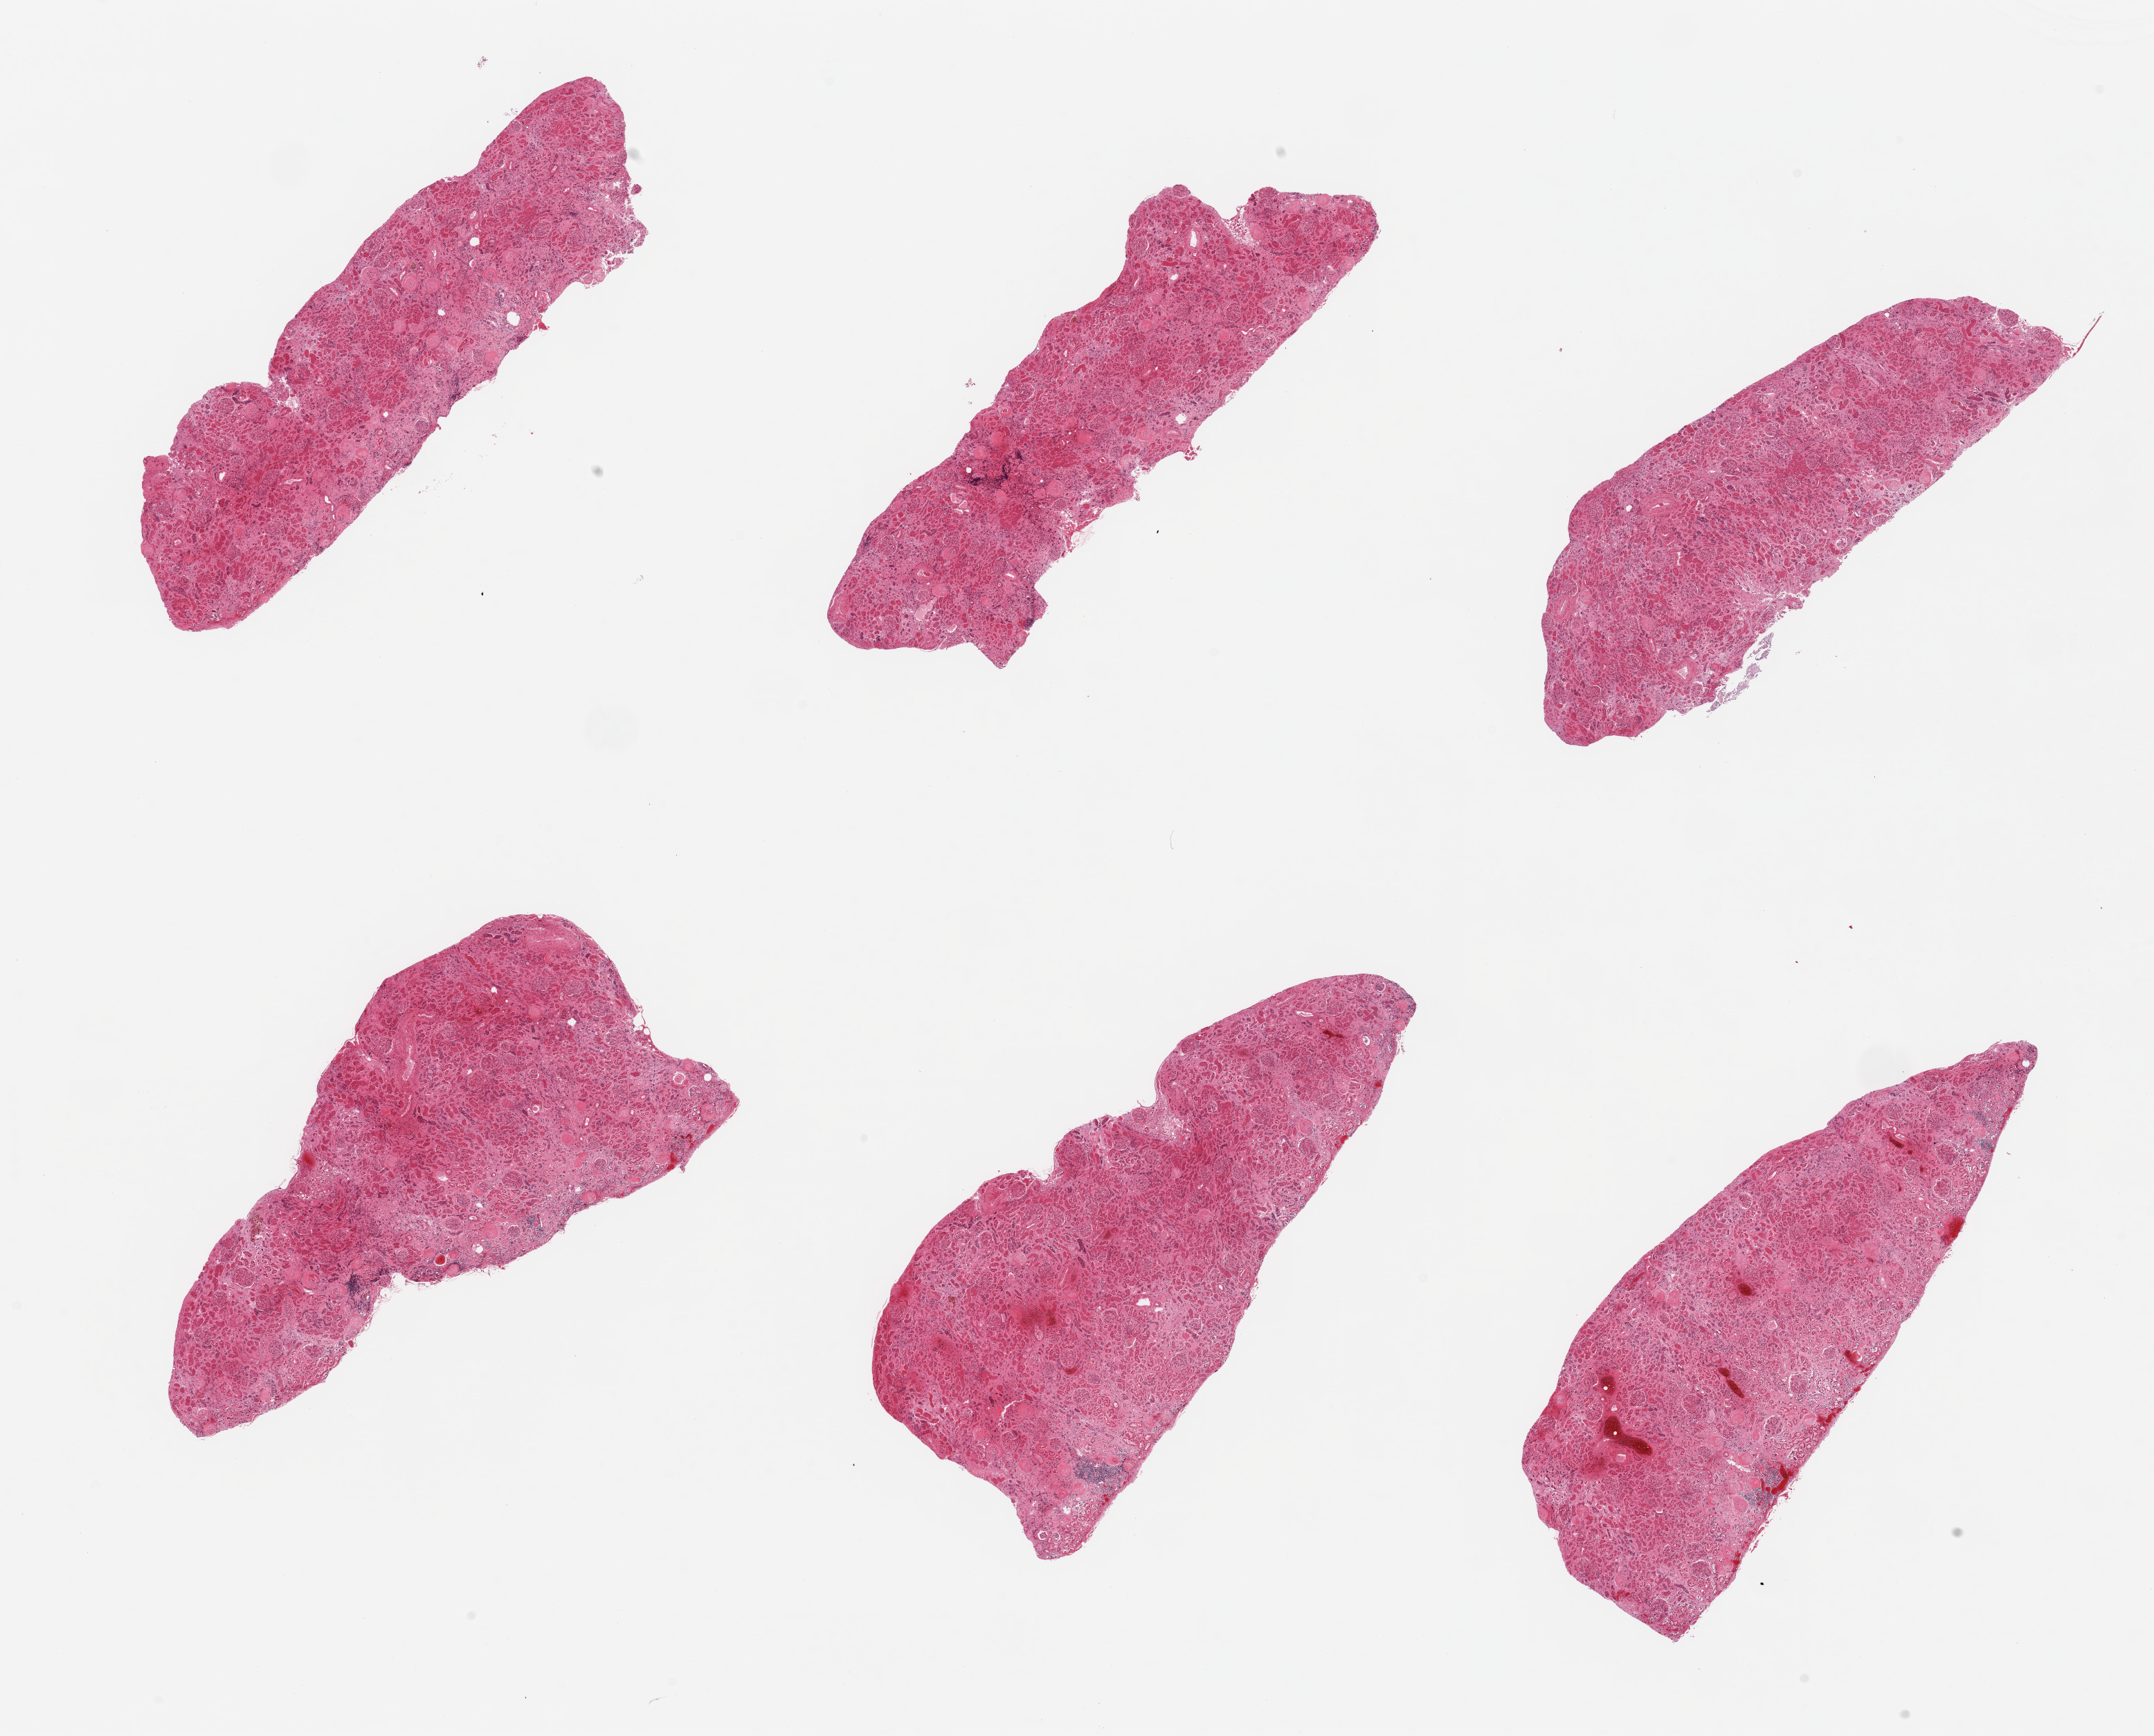
Haematoxylin and eosin whole-slide image, shown as a low-resolution overview of the whole scanned area (about 24.6 x 19.8 mm, from a 20x scan). PAXgene-fixed, paraffin-embedded tissue. Sampled site (target tissue): renal cortex. Donor tissue sample.
Reviewer comment on this tissue sample: 6 pieces; glomerulosclerosis, interstitial fibrosis, focal chronic inflammation, arteriosclerosis.